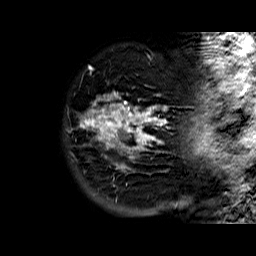
Breast MRI (dynamic contrast-enhanced), one sagittal slice; dynamic contrast-enhanced series, time point 2 of 6 at this slice position (early post-contrast); 1.5 T; TE 6.3 ms, TR 32.4 ms; 256 × 256 image matrix. Female patient. From the clinical record (not read from this slice): setting: breast cancer imaged before/during neoadjuvant chemotherapy; receptor status: HR-positive, HER2-negative.
Structures marked on this image (semi-automatically segmented with operator editing):
- analysis volume of interest (the breast-tissue region the enhancement analysis was run in; not a lesion): bounding box (x1, y1, x2, y2) in pixels: (79, 91, 171, 177)
- tumour enhancement mask (voxels above the 100 % enhancement threshold inside the analysis volume of interest): (79, 92, 167, 169)